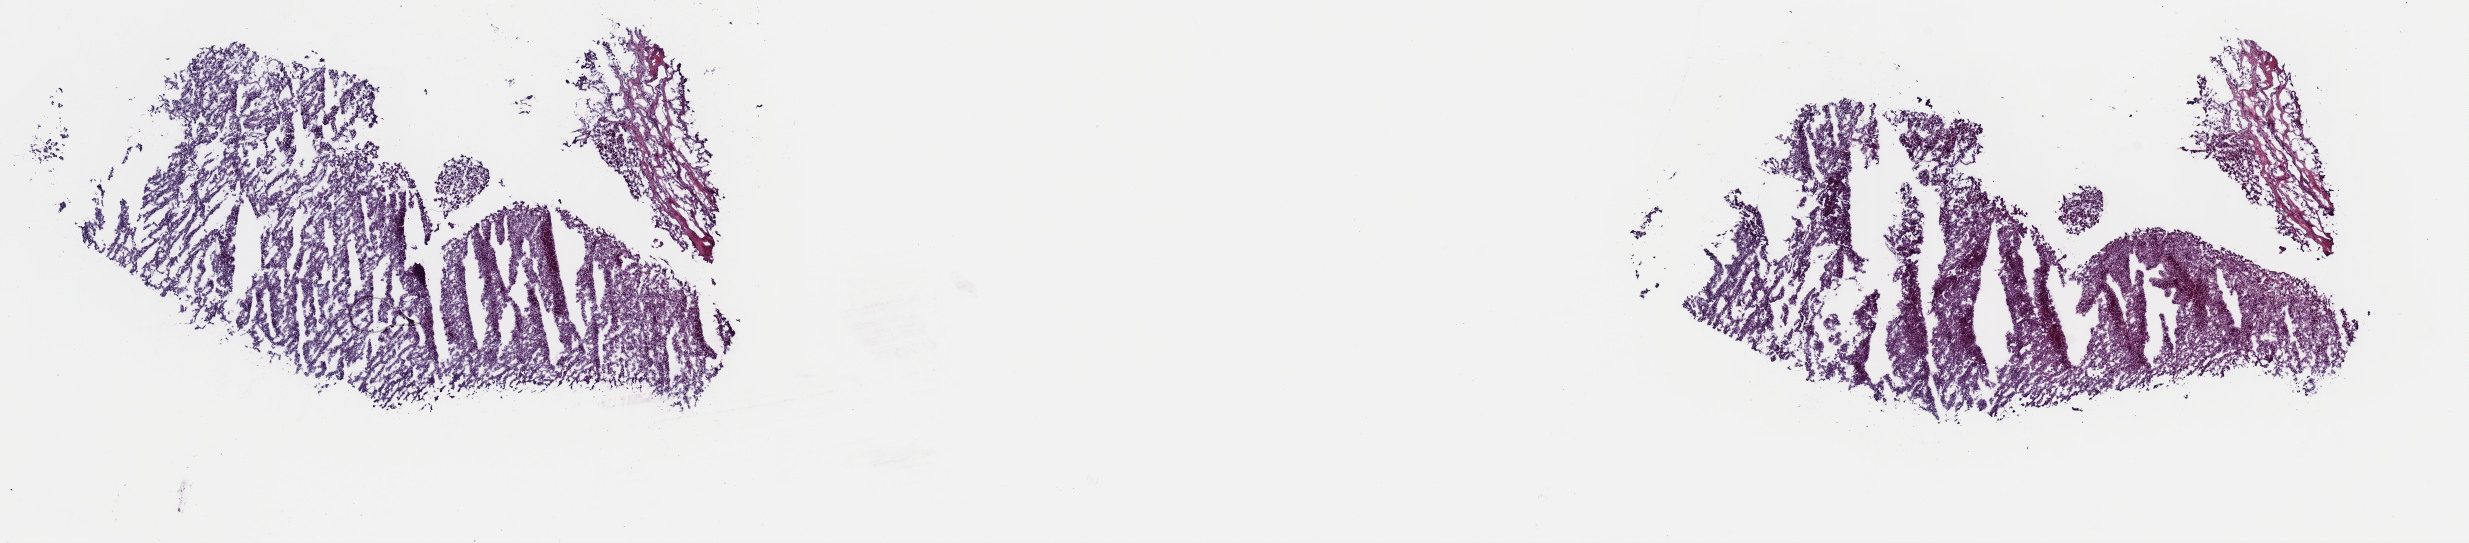
Whole-slide histology image, Hematoxylin and eosin (H&E) stained — shown as a low-resolution overview of the whole scanned area (about 19.5 x 4.3 mm); frozen section; sample: primary tumour, adrenal cortex. Patient: female, age at initial diagnosis 54 years. Slide review estimates, as recorded: tumour cells 95%, tumour nuclei 98%, normal cells 0%, stromal cells 5%, necrosis 0%. Infiltration values recorded for this section: lymphocyte infiltration 0%, monocyte infiltration 0%, neutrophil infiltration 0%.
Laterality: left. Histologic diagnosis: Adrenal cortical carcinoma (cortex of adrenal gland).